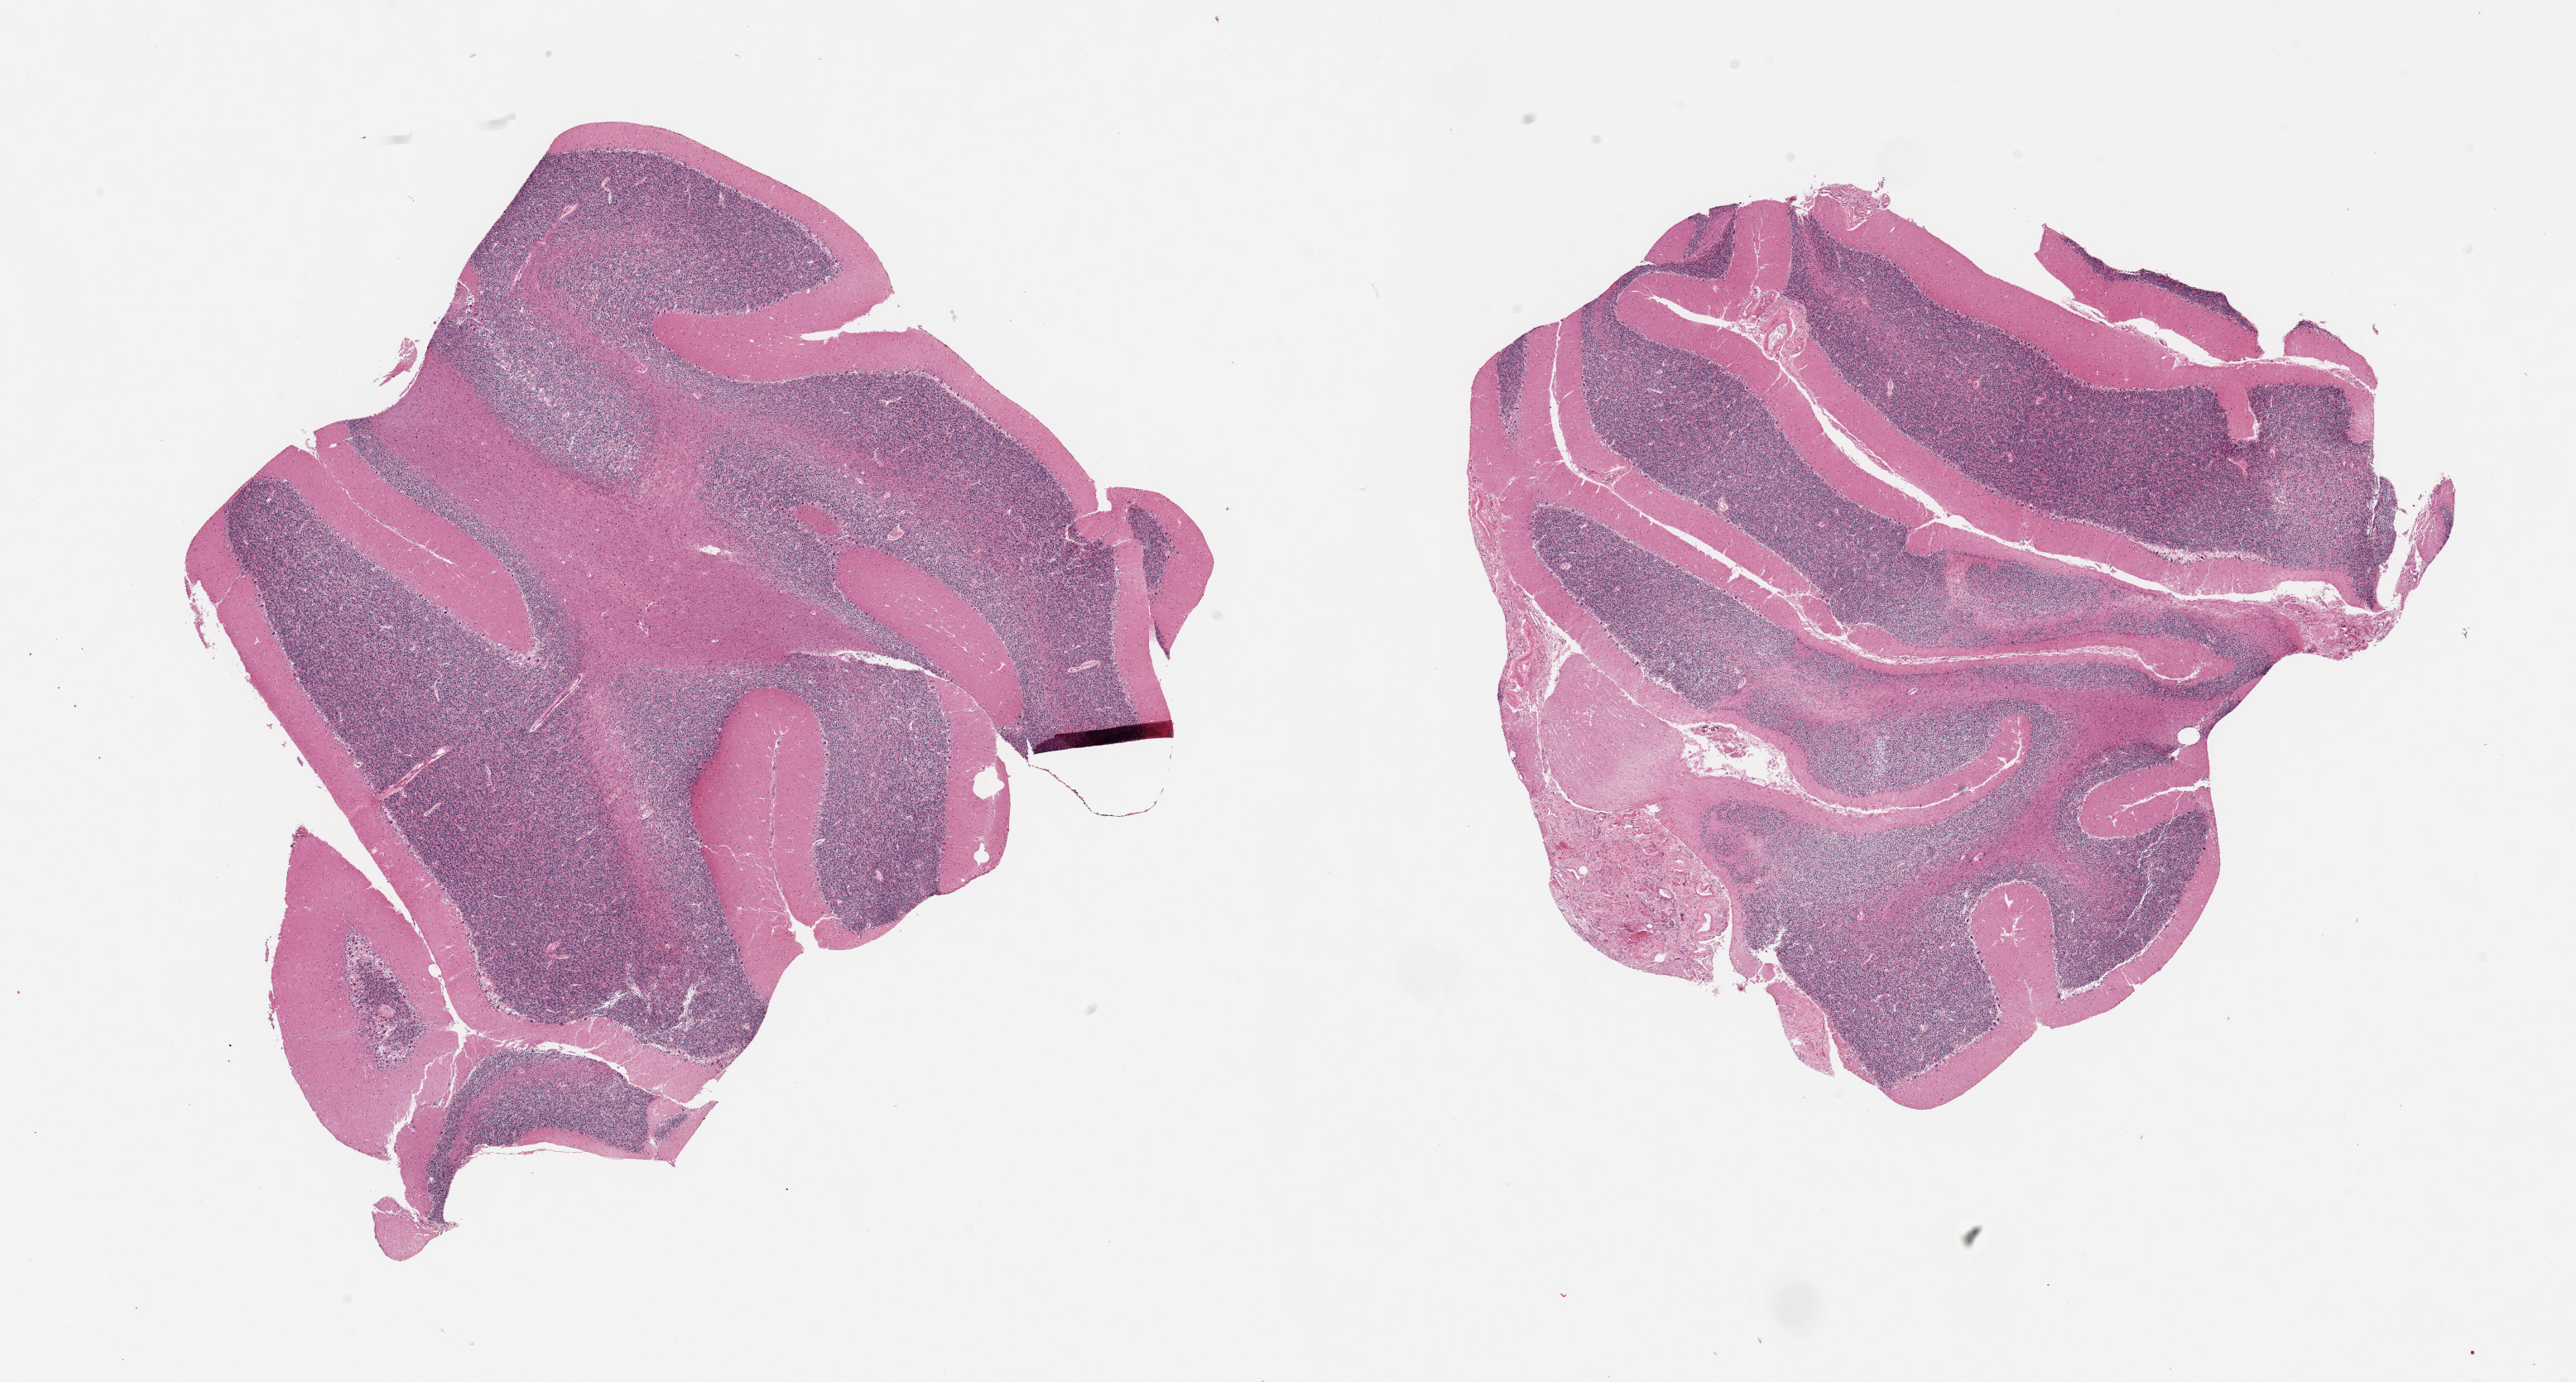
Digitized H&E-stained section — a low-resolution overview of the entire scanned area, about 24.6 x 13.2 mm; PAXgene-fixed paraffin-embedded (PFPE) section; target tissue: cerebellum; donor tissue sample. Male donor.
- review note (as recorded): 2 pieces, no abnormalities